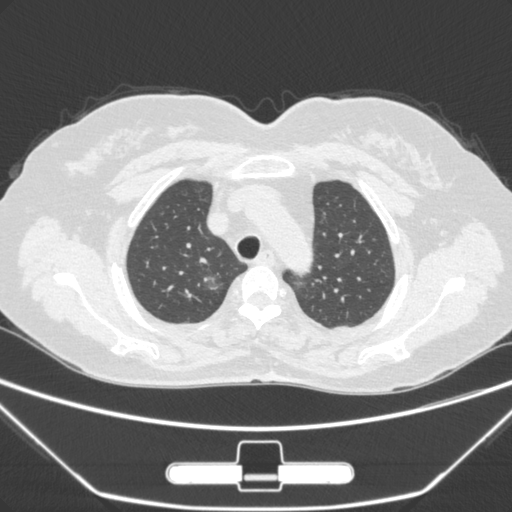
Chest CT, one axial slice. Position 225 of 275 along the scan axis. Lung window (W 1500 / L -600 HU). 512 × 512 image matrix. Patient: female, 63 years. Case-level facts recorded for this patient, not image findings: clinical TNM (as recorded): T1a N0 M0; histopathological grade: G1.
Annotated regions visible in this slice (rectangle marked by the reading radiologist):
- lung tumour (recorded histology: adenocarcinoma): bounding box [x1, y1, x2, y2] px = [195, 262, 228, 291]